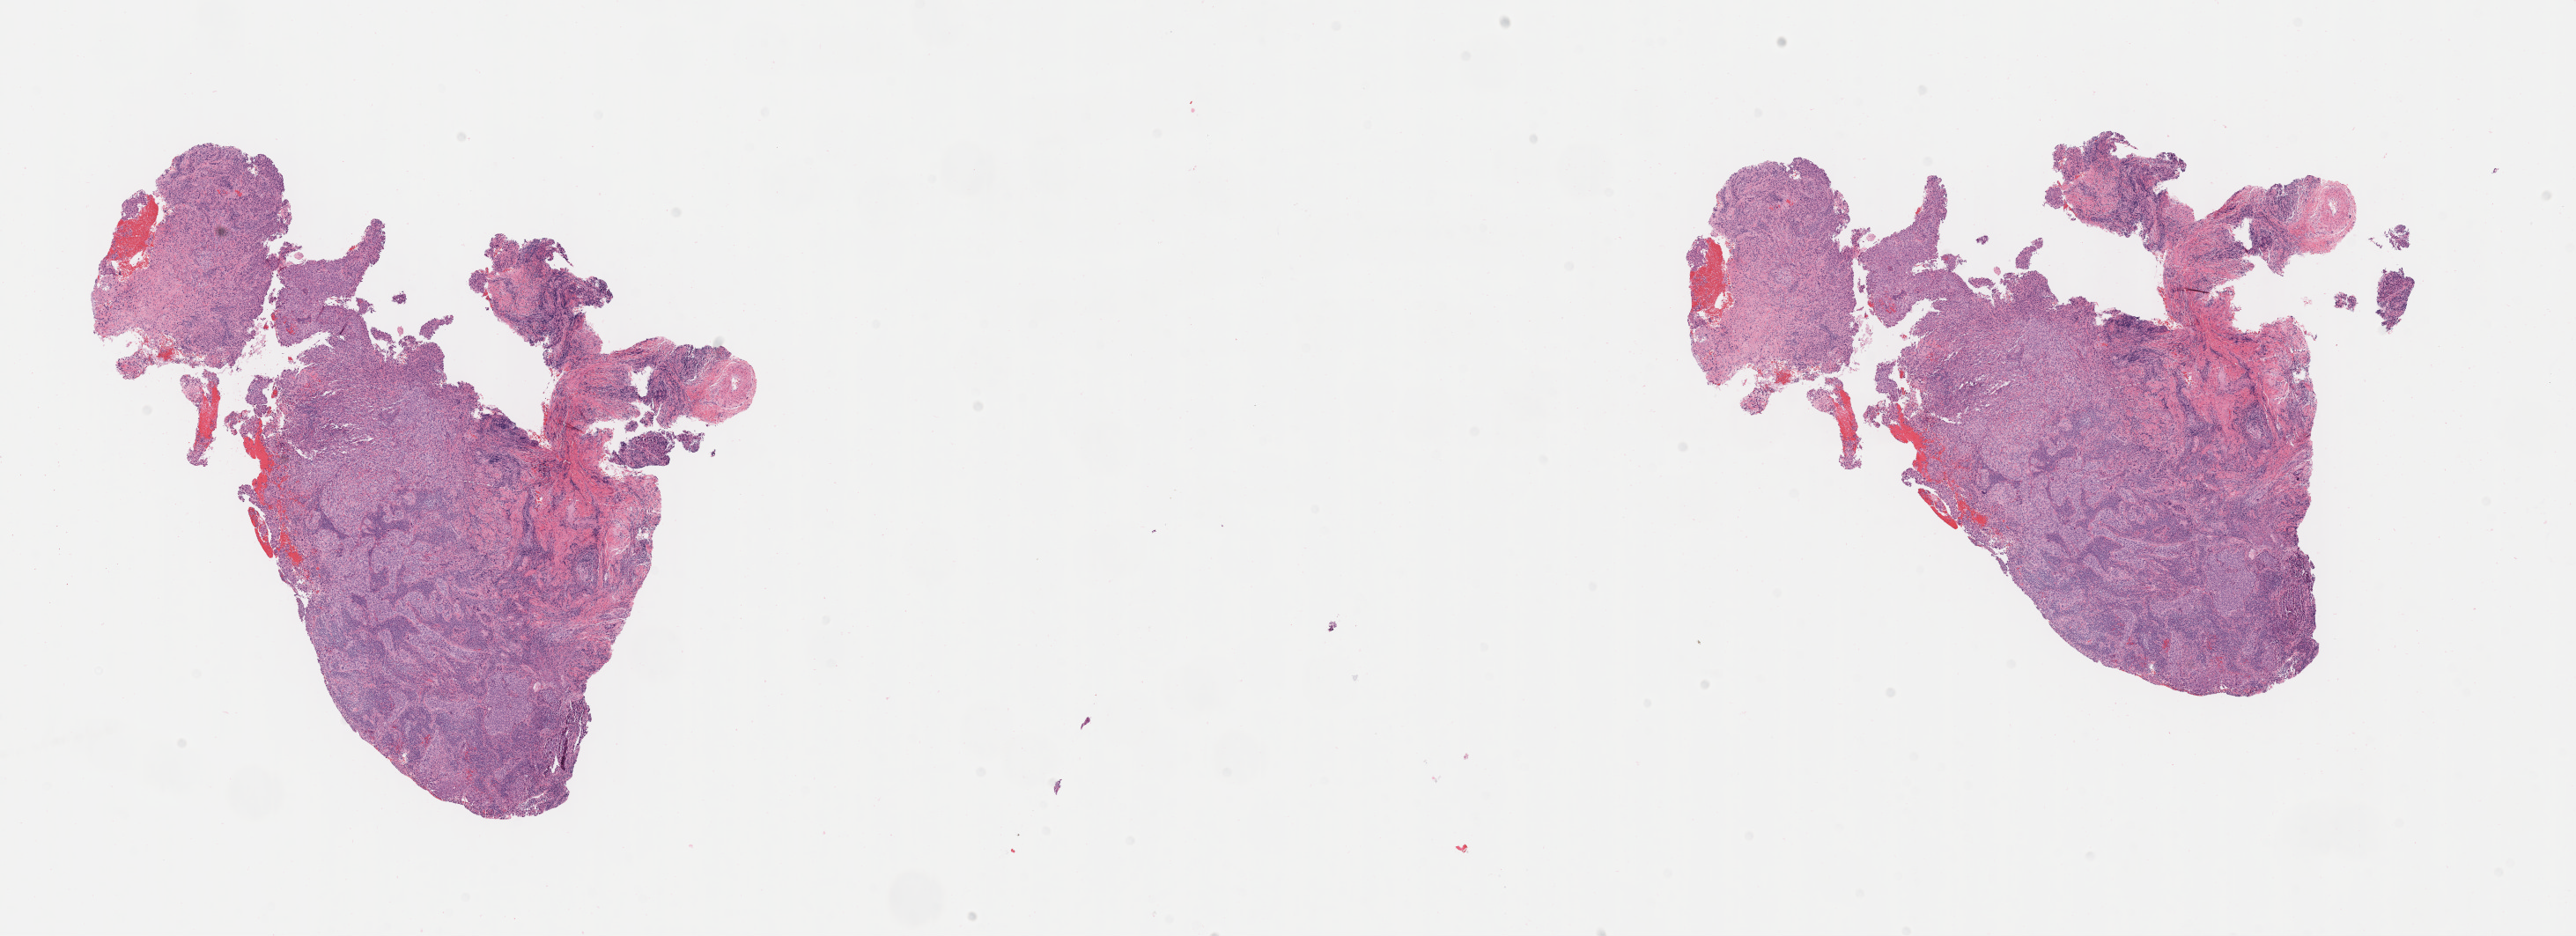
Digitized H&E-stained section — low-resolution overview of the scanned area, about 23.7 x 8.6 mm; tumor tissue; anatomic site: cervix. Patient female; age 35 years.
Histologic diagnosis: Squamous cell carcinoma, large cell, nonkeratinizing, NOS.